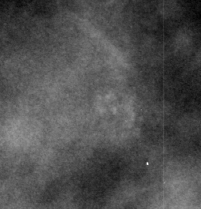
Region of interest cut from a scanned film mammogram (one marked finding), right breast, MLO view, BI-RADS breast density category 3 (scale 1–4).
Finding: calcifications, morphology amorphous, distribution clustered; BI-RADS assessment category 3; pathology (as recorded): benign.